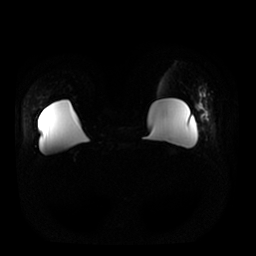
Breast MRI, one axial slice. Slice 6 of 25 in the series (ordered by position). Diffusion-weighted series; image 2 of 4 stored at this slice position (different b-values; order by instance number). 1.5 T. 4 mm slice thickness. 256 × 256 image matrix, field of view 380 × 380 mm. Female patient.
Structures marked on this image (expert manual segmentation):
- tumour on diffusion-weighted imaging: bounding box <198,101,206,121> (left, top, right, bottom; pixels)